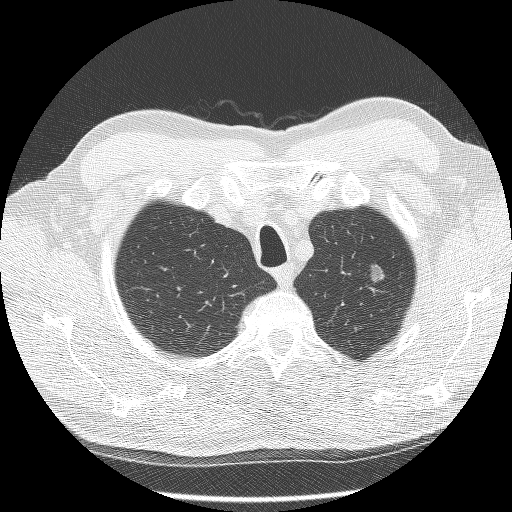
Chest CT (low-dose screening protocol), one axial image; second annual screen; lung window (W 1500 / L -600 HU); 2.5 mm slice thickness; lung (sharp) reconstruction kernel (BONE); 512 × 512 image matrix. Male, age 60 years at enrolment. Former smoker at enrolment.
Expert reader's lesion annotation, box from (x=346, y=256) to (x=399, y=299) px. The screening reader recorded 2 non-calcified nodules or masses ≥4 mm on this exam (right lower lobe, left upper lobe); which of them this box marks is not recorded. Later outcome: lung cancer diagnosed 448 days after this screen — bronchiolo-alveolar carcinoma, non-mucinous, left upper lobe, well differentiated (G1), stage IA (AJCC 6th edition), 16 mm at pathology.